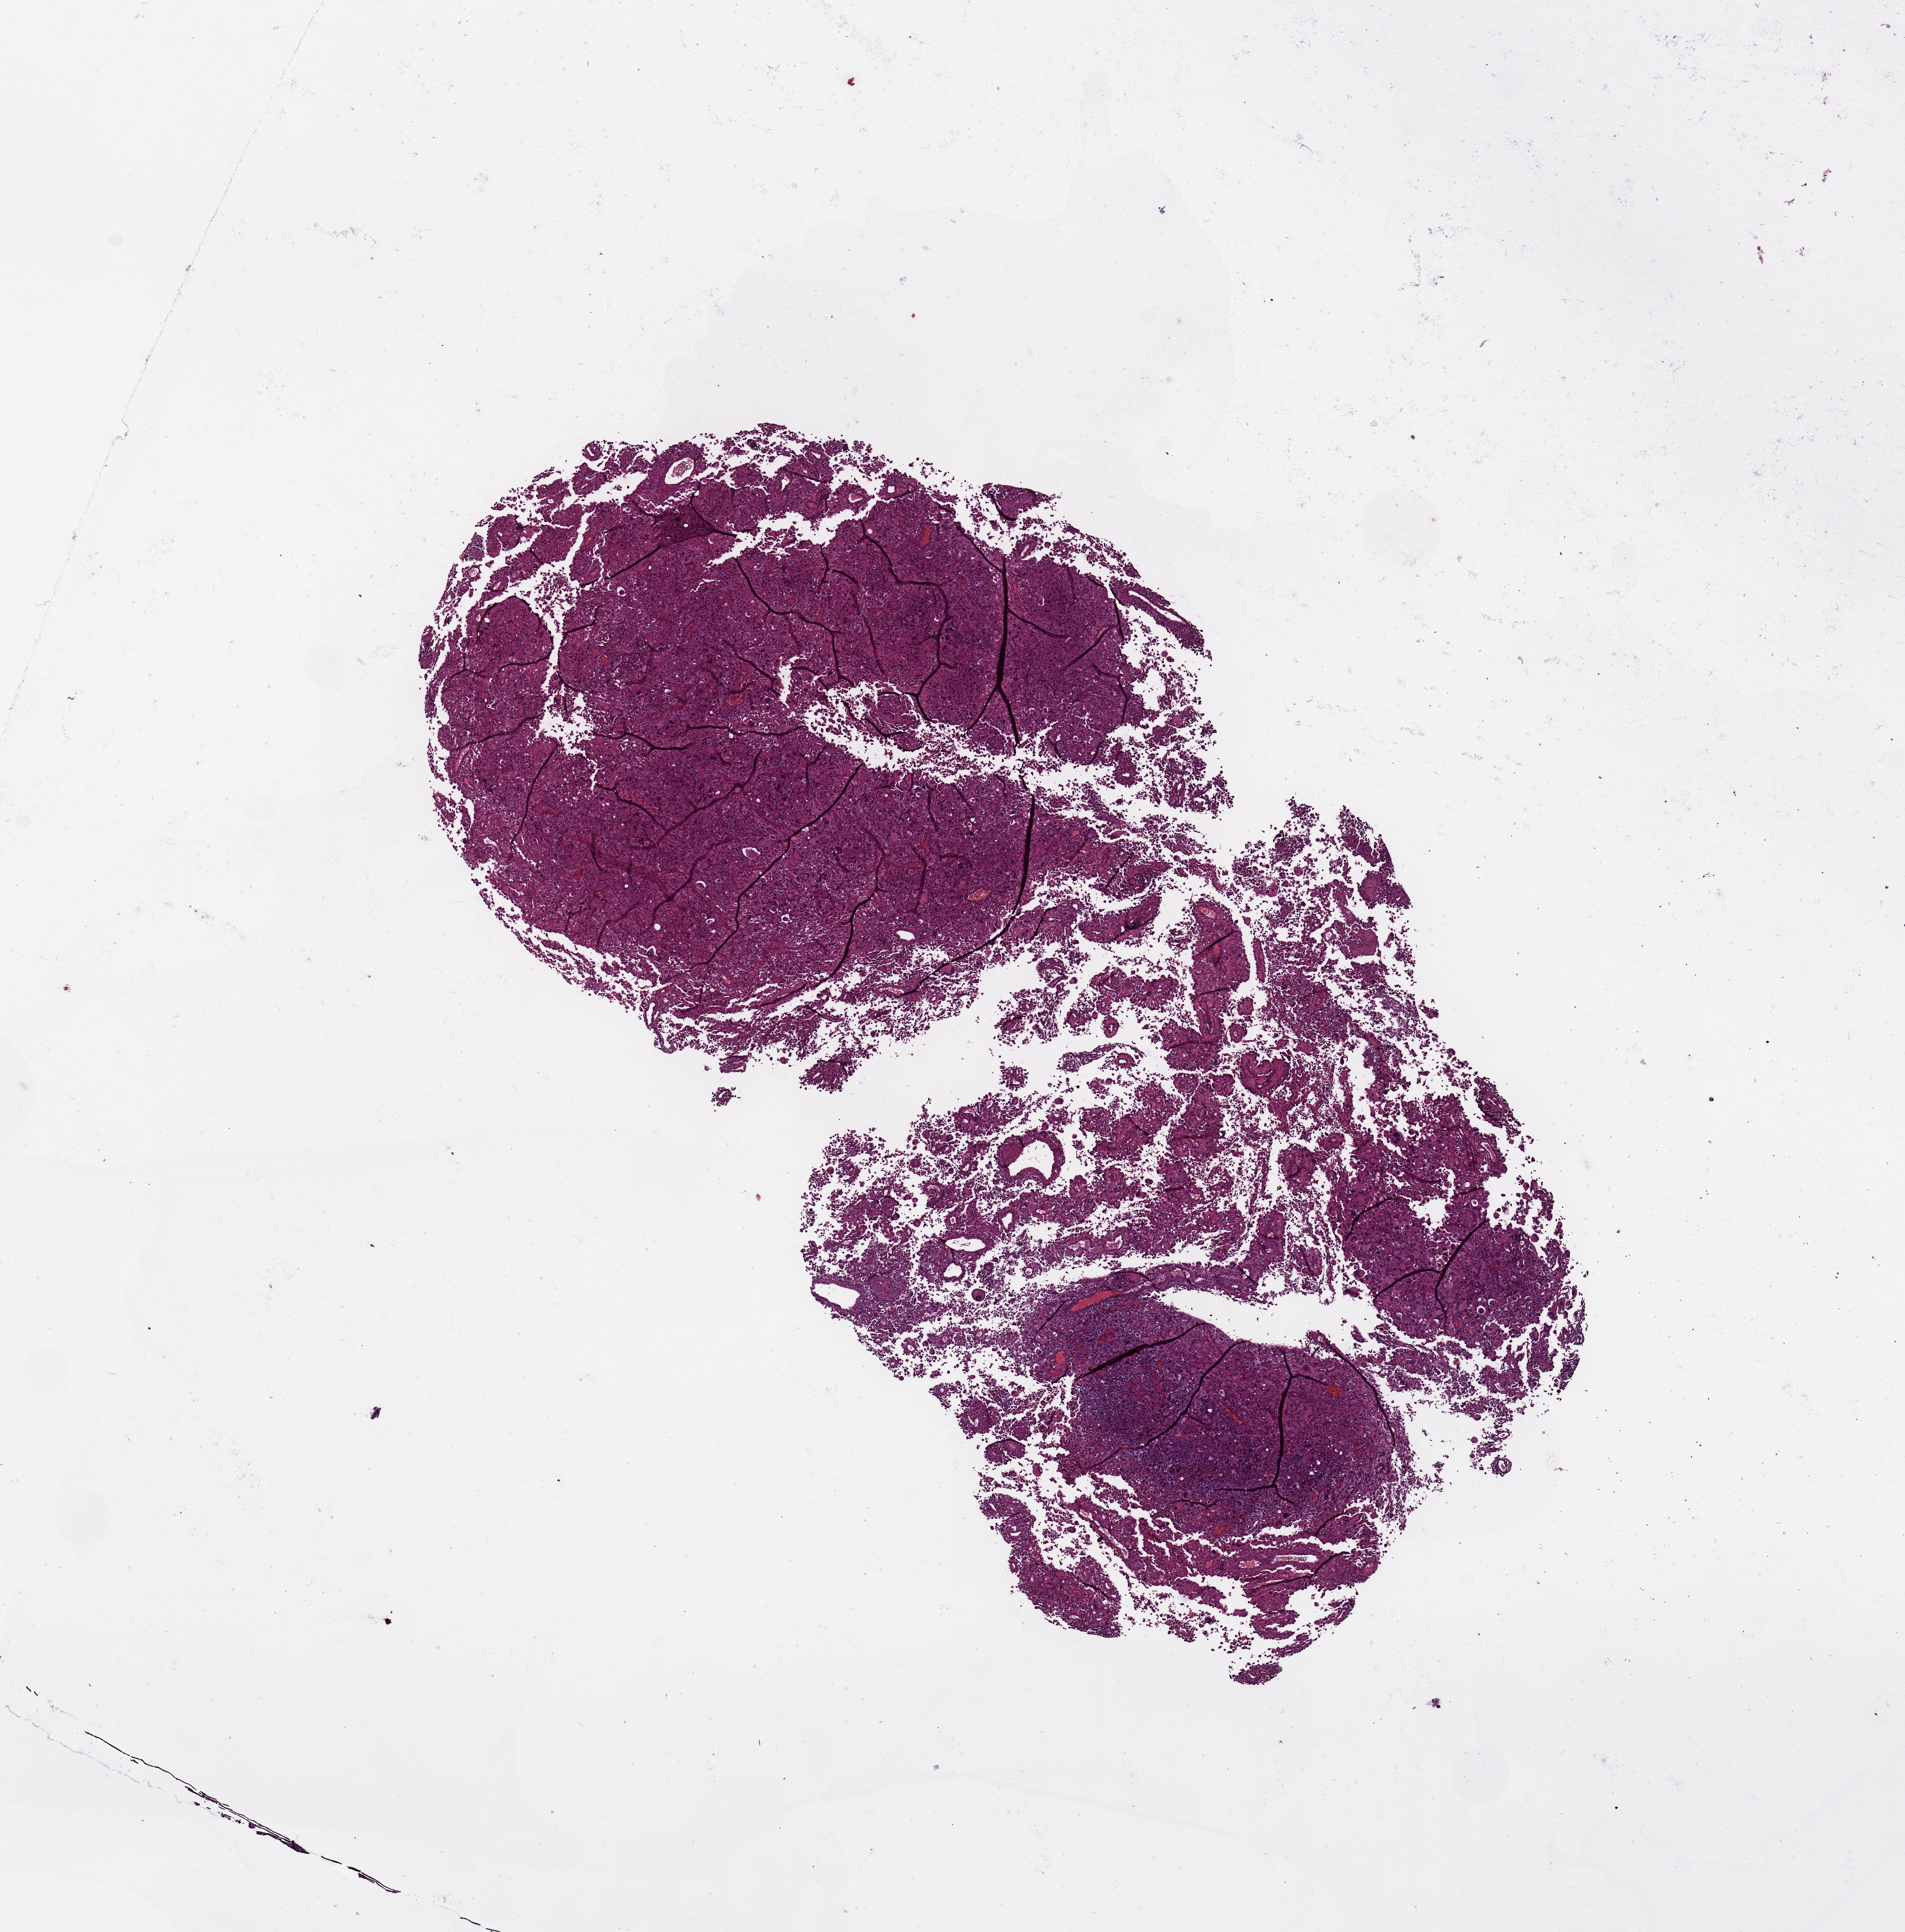
Digitized H&E tissue section (whole slide), whole scanned area (about 11.8 x 12.0 mm, from a 20x scan) shown as a low-resolution overview, tumour tissue sample, sampled site: brain. 47-year-old male patient. Slide review estimates, as recorded: tumour nuclei 80%, necrosis 10%.
Diagnosis: Glioblastoma.